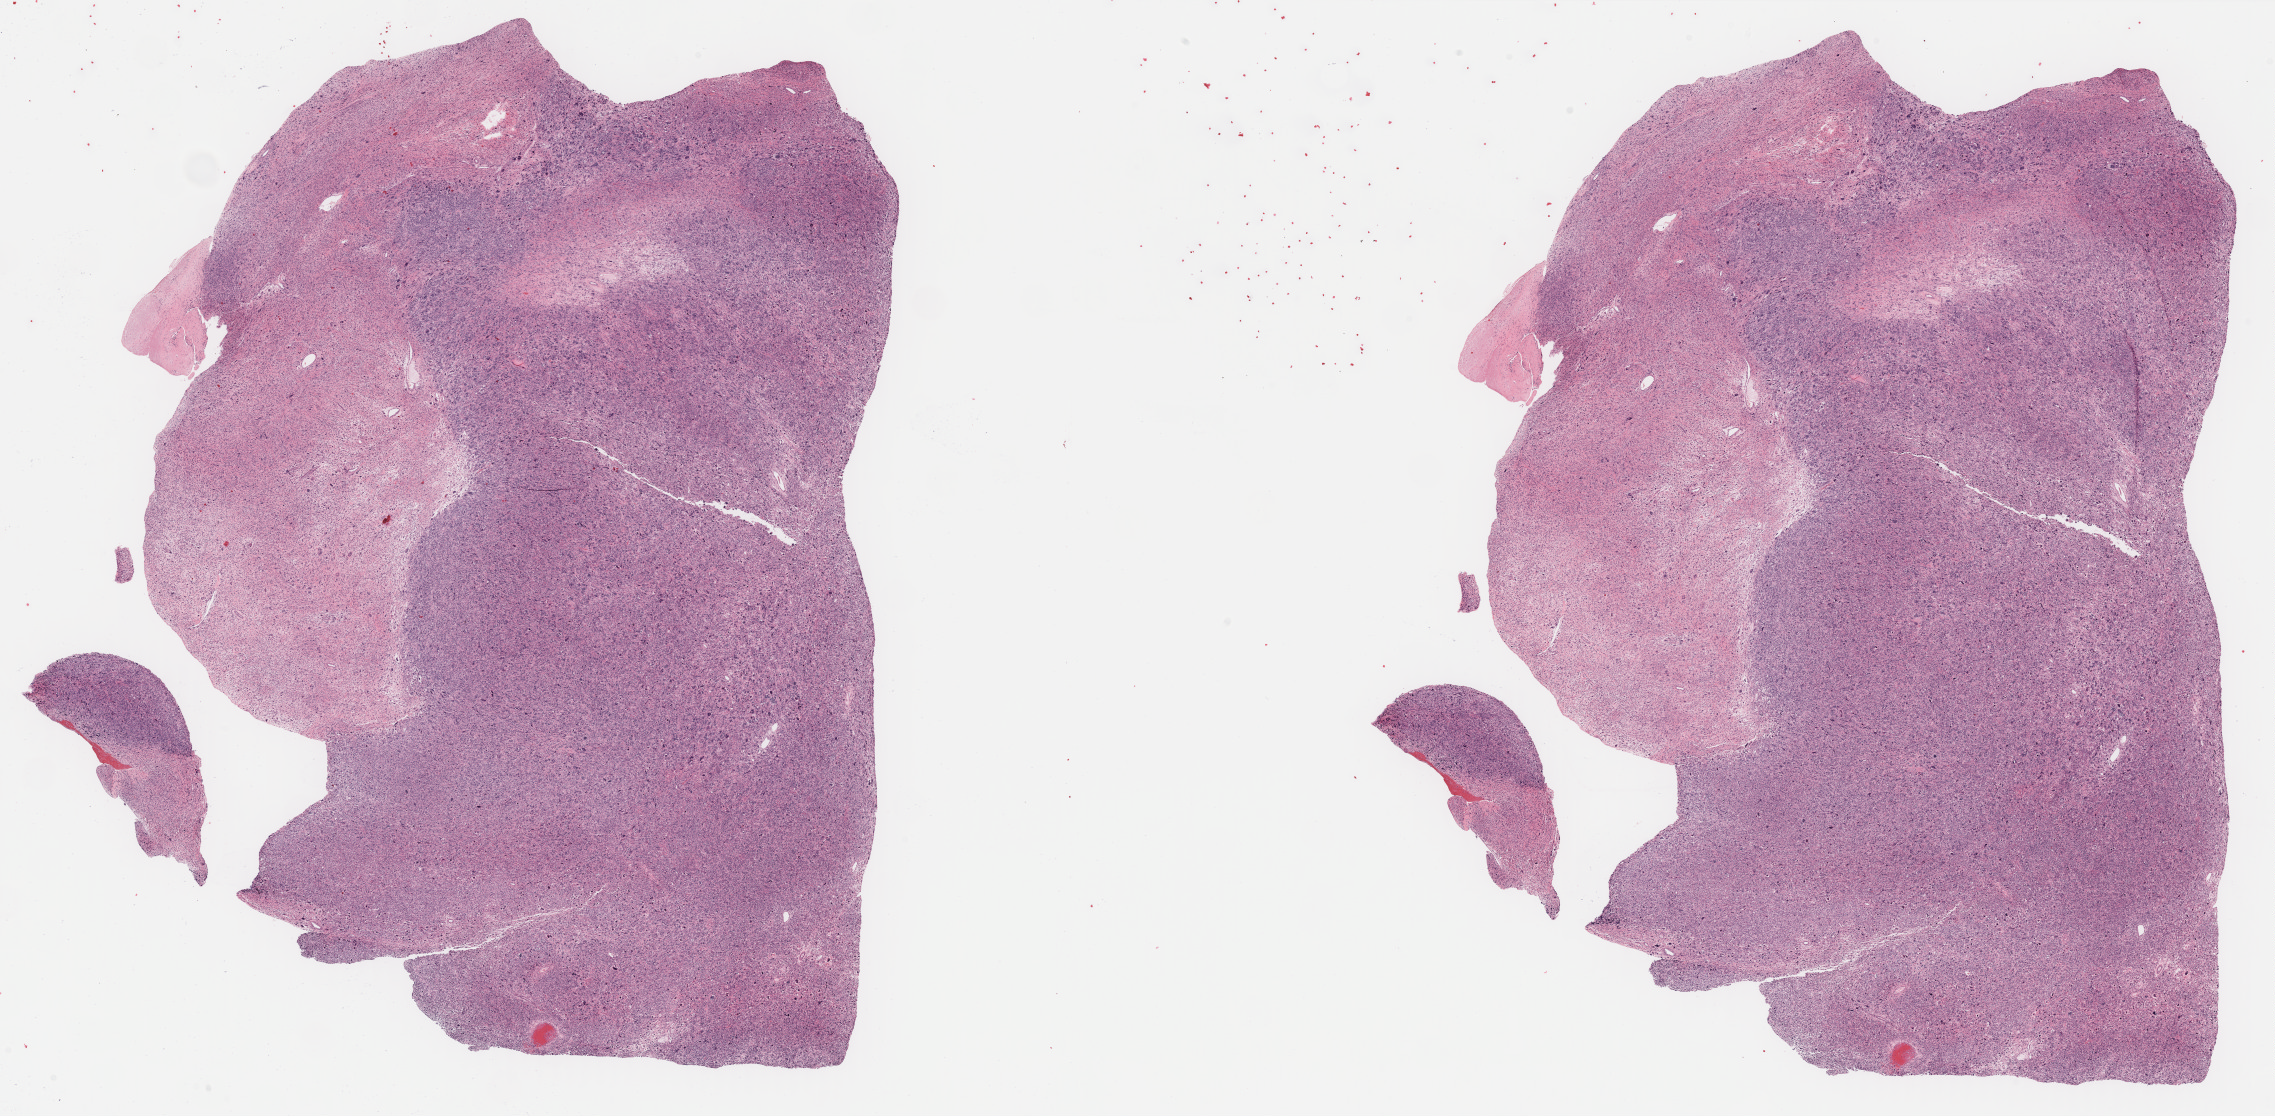
Digitized Hematoxylin and eosin (H&E) stained tissue section (whole slide) — whole scanned area (about 36.0 x 17.7 mm, slide scanned at 40x) shown as a low-resolution overview. FFPE section. Sample: primary tumour, uterus. Female, age 58 years at initial diagnosis.
• pathologic diagnosis: Leiomyosarcoma, NOS